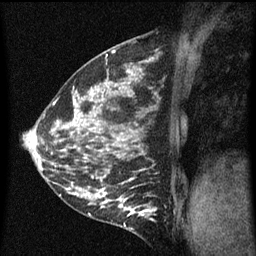
Breast MRI (dynamic contrast-enhanced), one sagittal slice; slice 21 of 60 in the series (ordered by position); dynamic contrast-enhanced series, image 2 of 5 at this slice position (ordered by acquisition); 1.5 T; TE 4.2 ms, TR 8 ms; 2 mm slice thickness; 256 × 256 image matrix. Patient: female, 35 years.
Outlined on this slice (semi-automatic segmentation, software-assisted and operator-edited):
- analysis volume of interest (the breast-tissue region the enhancement analysis was run in; not a lesion): bounding box (x1, y1, x2, y2) in pixels: (118, 194, 158, 229)
- tumour enhancement mask (voxels above the 70 % enhancement threshold inside the analysis volume of interest): (119, 200, 157, 227)